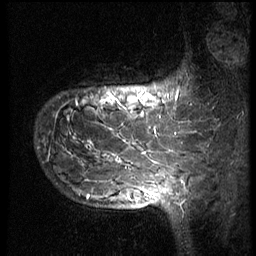
Breast MRI (dynamic contrast-enhanced), one sagittal slice. Slice 16 of 66 in the series (ordered by position). 3 images stored at this slice position (order not interpretable as contrast timing). 1.5 T. TE 4.2 ms, TR 8.9 ms. 2.5 mm slice thickness. 256 × 256 image matrix, field of view 200 × 200 mm. Female patient, age 39 years. Case-level facts recorded for this patient, not image findings: setting: breast cancer imaged before/during neoadjuvant chemotherapy; receptor status: HER2-positive.
Structures marked on this image (semi-automatic segmentation, software-assisted and operator-edited):
- analysis volume of interest (the breast-tissue region the enhancement analysis was run in; not a lesion): box from (x=35, y=64) to (x=166, y=196) px
- tumour enhancement mask (voxels above the 140 % enhancement threshold inside the analysis volume of interest): (x=77, y=92)–(x=158, y=195)